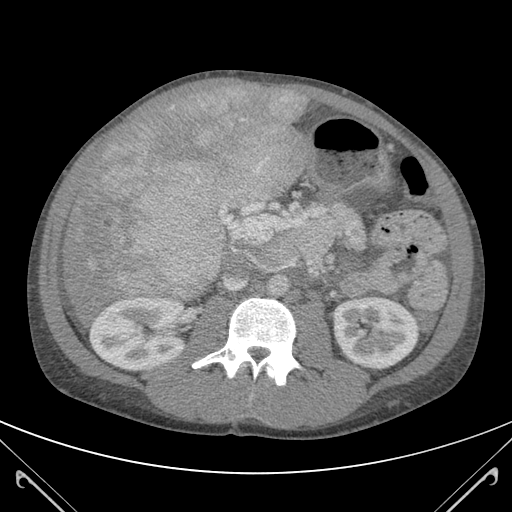
Contrast-enhanced abdominal CT (liver protocol), one axial slice; position 52 of 118 along the scan axis; 120 kVp; soft-tissue window (W 400 / L 40 HU); 3 mm slice thickness; 512 × 512 image matrix. Case-level facts recorded for this patient, not image findings: diagnosis: hepatocellular carcinoma (patient treated with transarterial chemoembolisation; whether this scan precedes or follows treatment is not stated here); TNM stage (as recorded): Stage-IIIB; Child-Pugh class: A.
Structures marked on this image (semi-automatically segmented with operator editing):
- abdominal aorta: bounding box [x1, y1, x2, y2] px = [268, 277, 288, 296]
- liver parenchyma outside the tumour (the mass and vessels are separate outlines, so this box may not span the whole liver): [58, 83, 315, 321]
- mass: [84, 87, 309, 301]
- liver vessels: [120, 216, 225, 287]